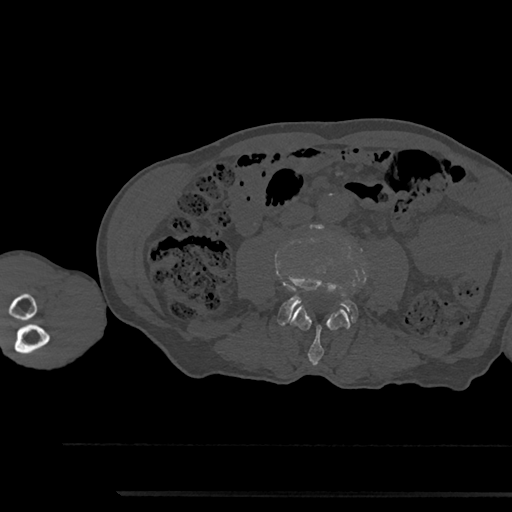
CT including the spine, one axial slice. Position 450 of 797 along the scan axis. 120 kVp. Bone window (W 1800 / L 400 HU). 512 × 512 image matrix, field of view 367 × 367 mm. Patient: male, 79 years. From the clinical record (not read from this slice): primary cancer: prostate.
Outlined on this slice (semi-automatically segmented with operator editing):
- L3 vertebra: bounding box (x1, y1, x2, y2) in pixels: (290, 305, 350, 365)
- L4 vertebra: (278, 276, 358, 326)